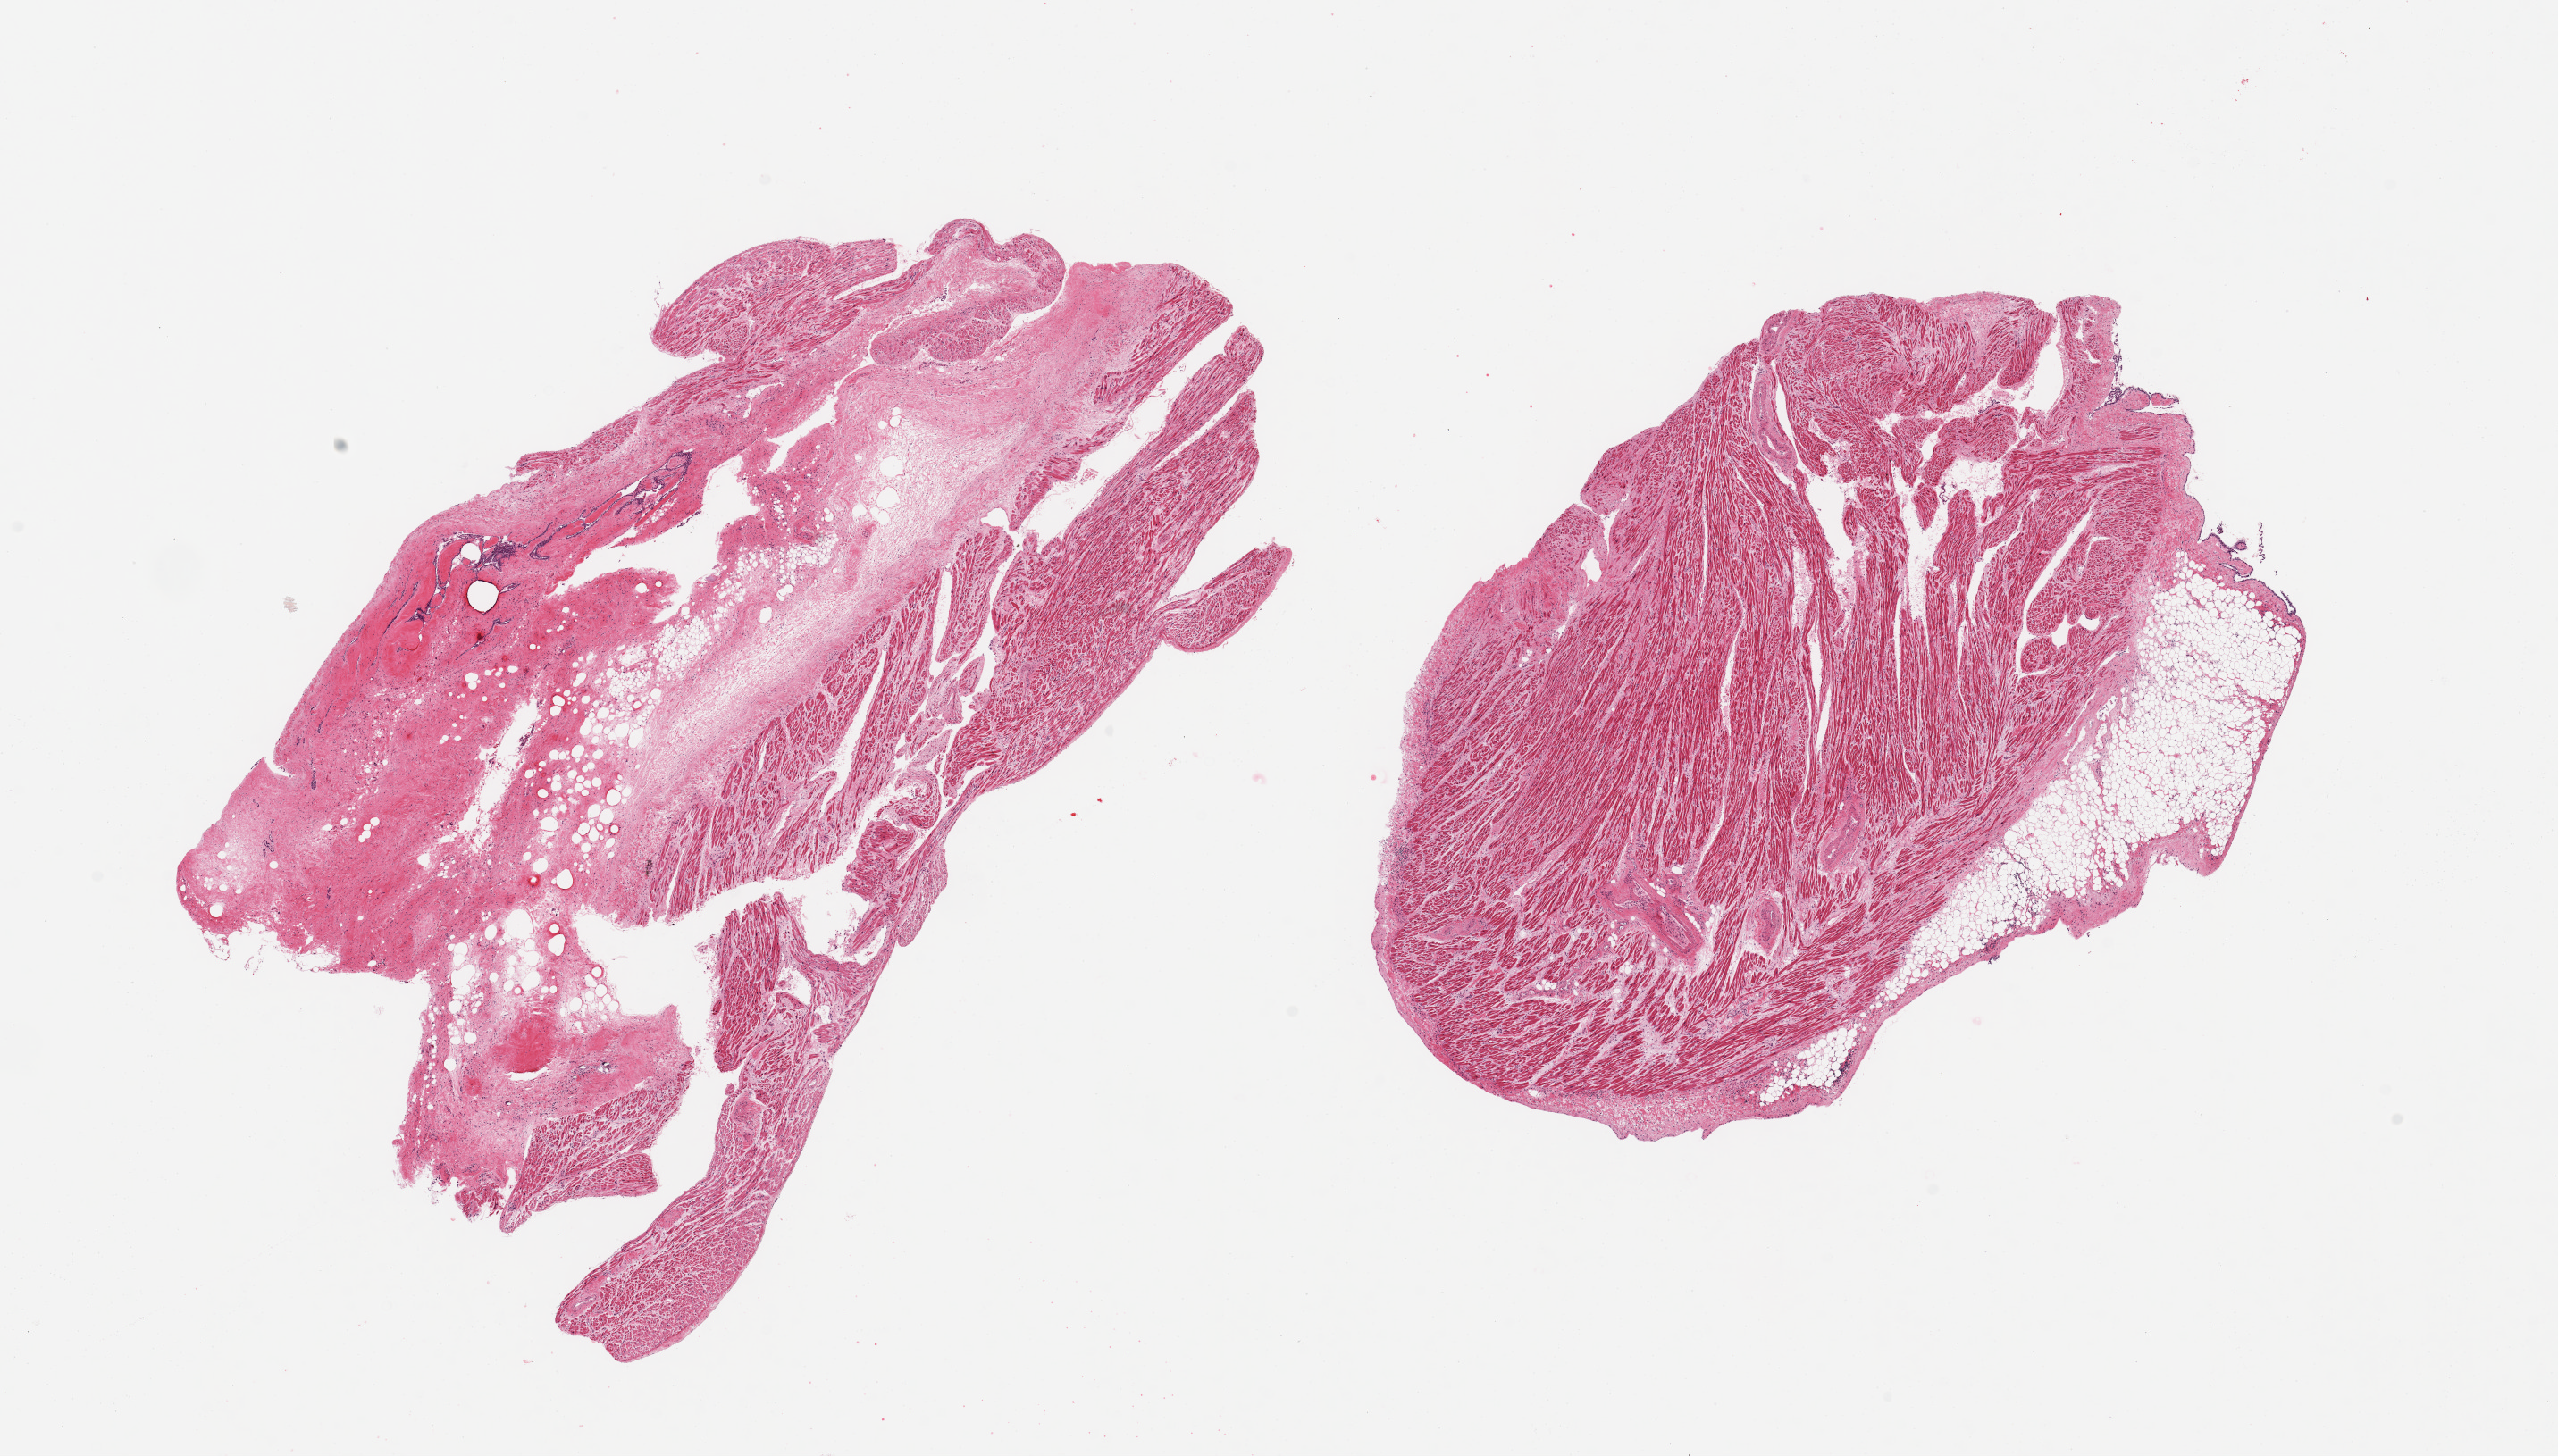
Digitized haematoxylin and eosin-stained section — a low-resolution overview of the entire scanned area, about 22.6 x 12.9 mm (slide scanned at 20x); PAXgene-fixed paraffin-embedded (PFPE) section; target tissue: auricular appendage; tissue donor sample. Donor sex: female.
Pathologist's review note for this sample: 2 pieces; one is ~15% fat, 2nd is ~60% fat/fibrous with scar, suture material, and focal foreign body giant cell reaction (history of CABG), hypertrophy.